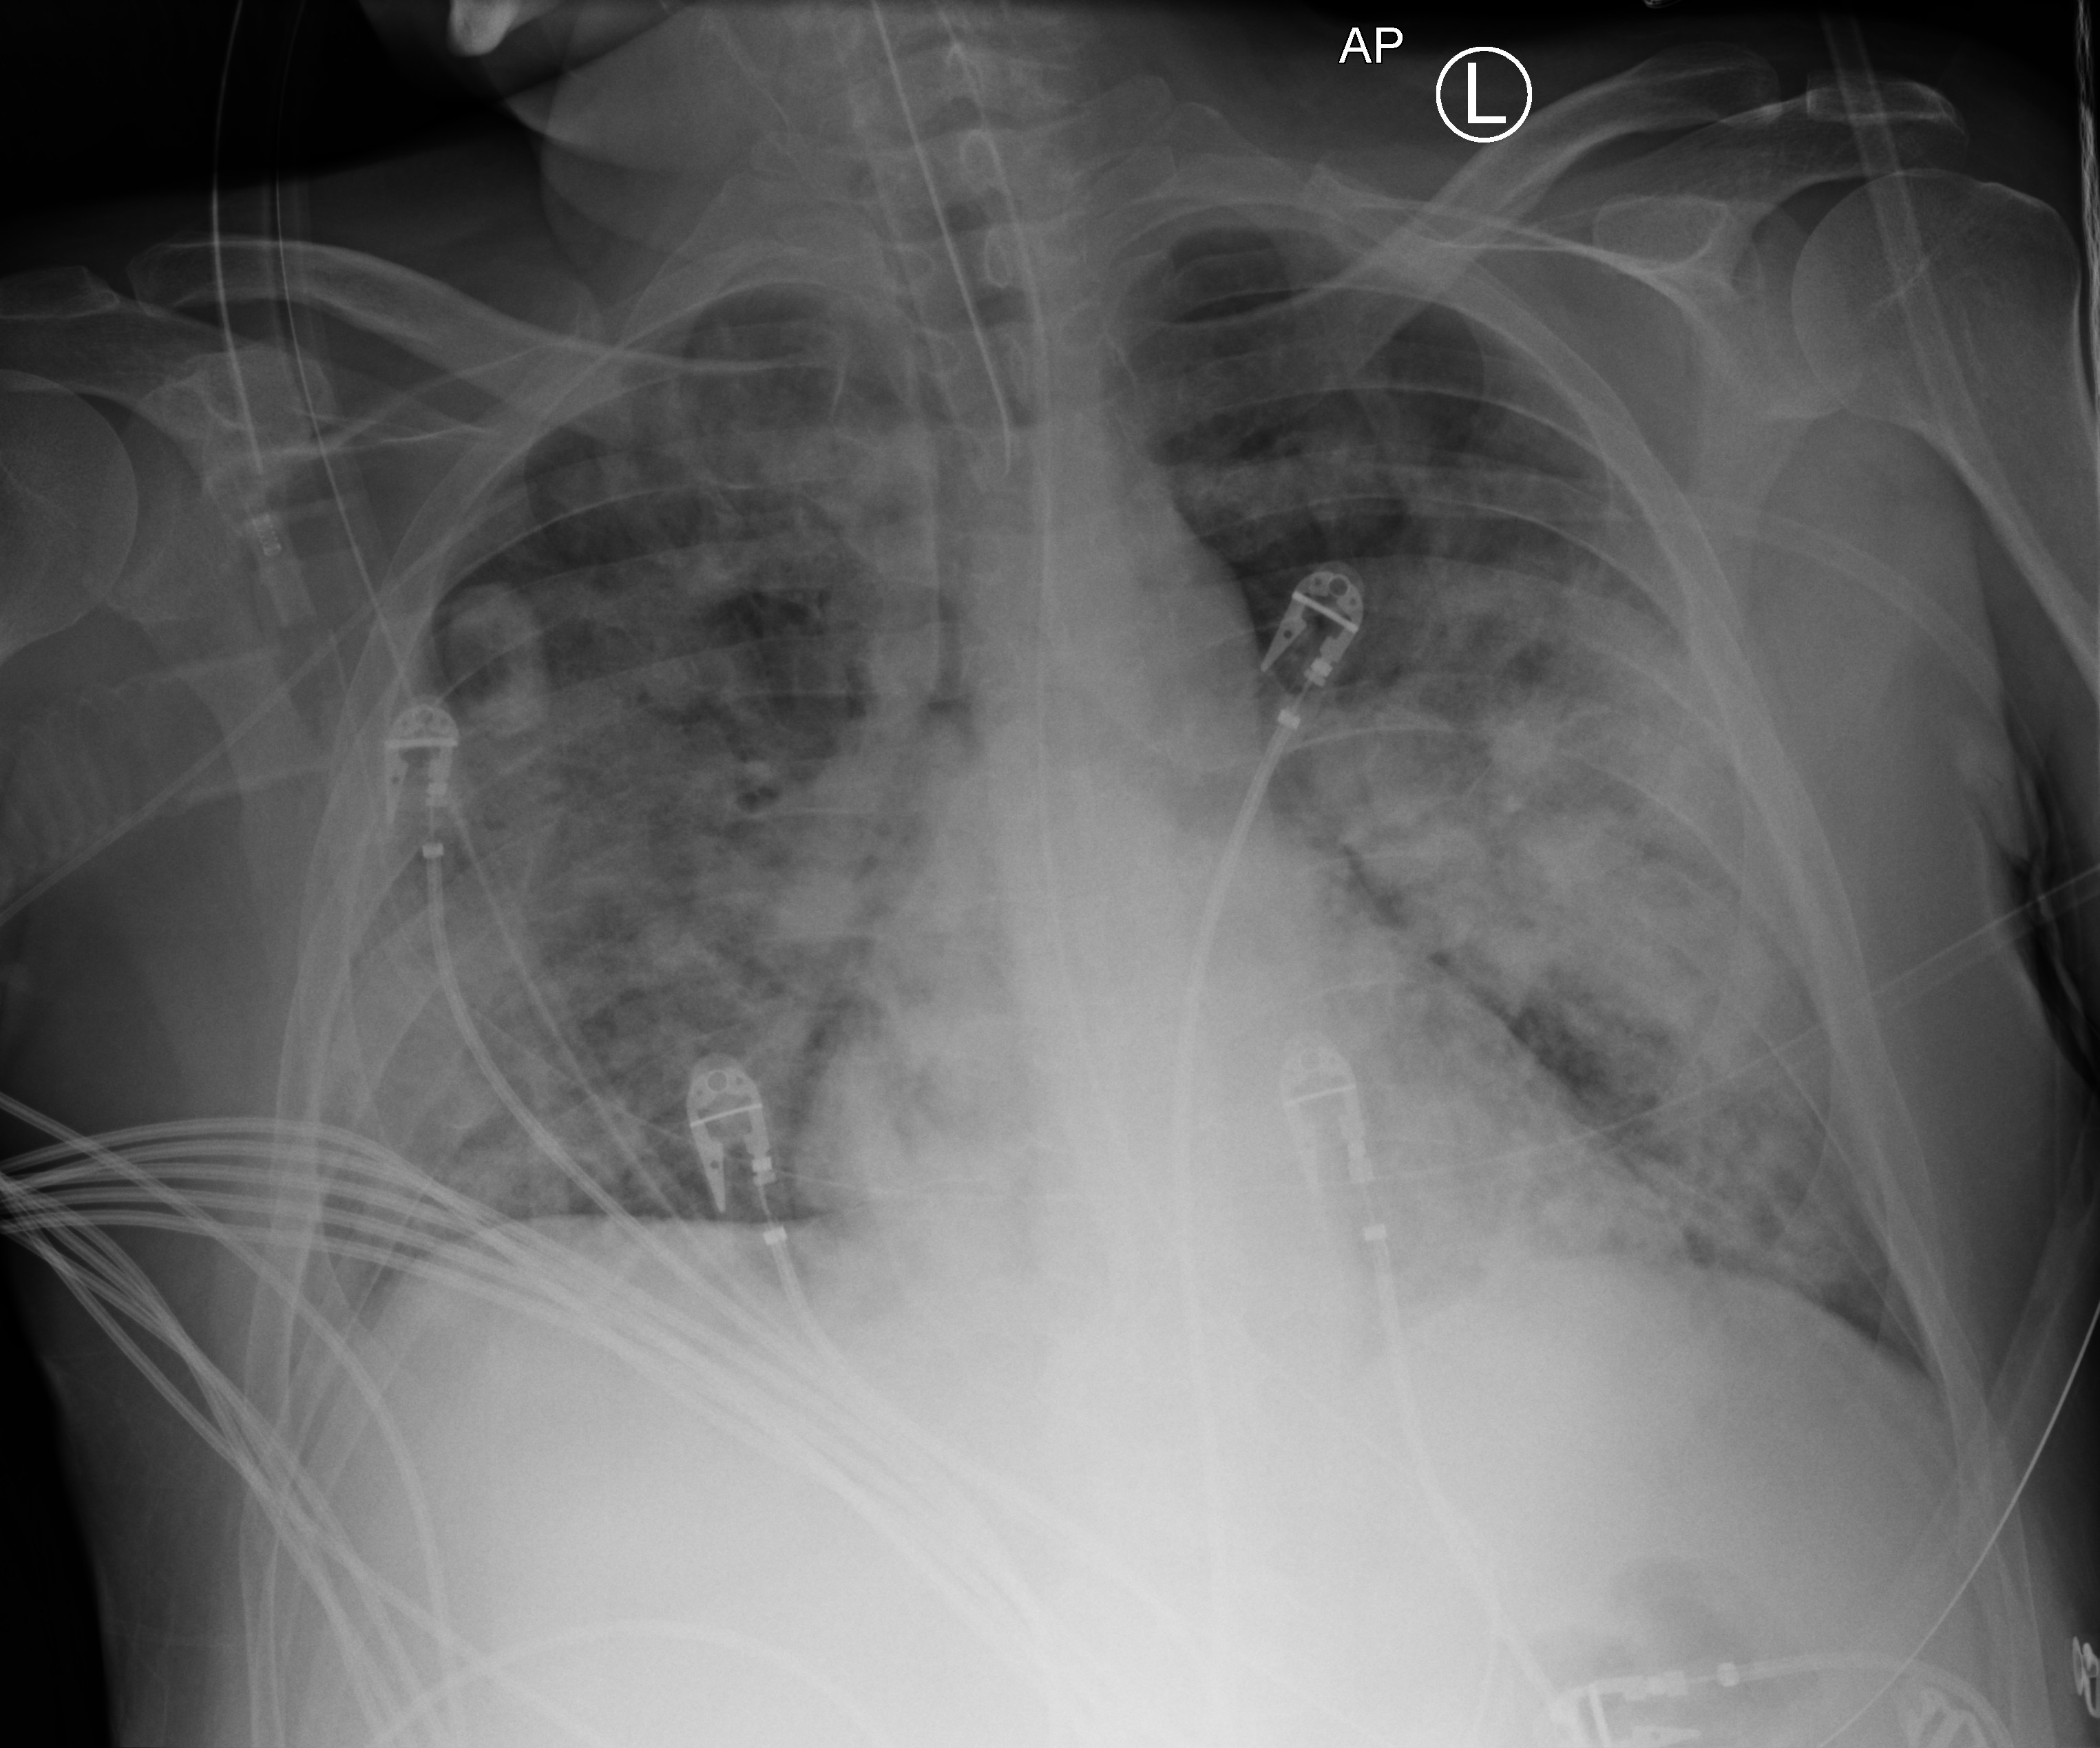
Portable chest radiograph; anteroposterior (AP) projection. Male patient hospitalised with COVID-19, age 18–59 years.
Admission-level facts for this patient (not findings on this image; timing relative to this image not recorded): other chronic lung disease (admission record): no; admitted to intensive care during this hospital stay: yes; hypertension (admission record): no.